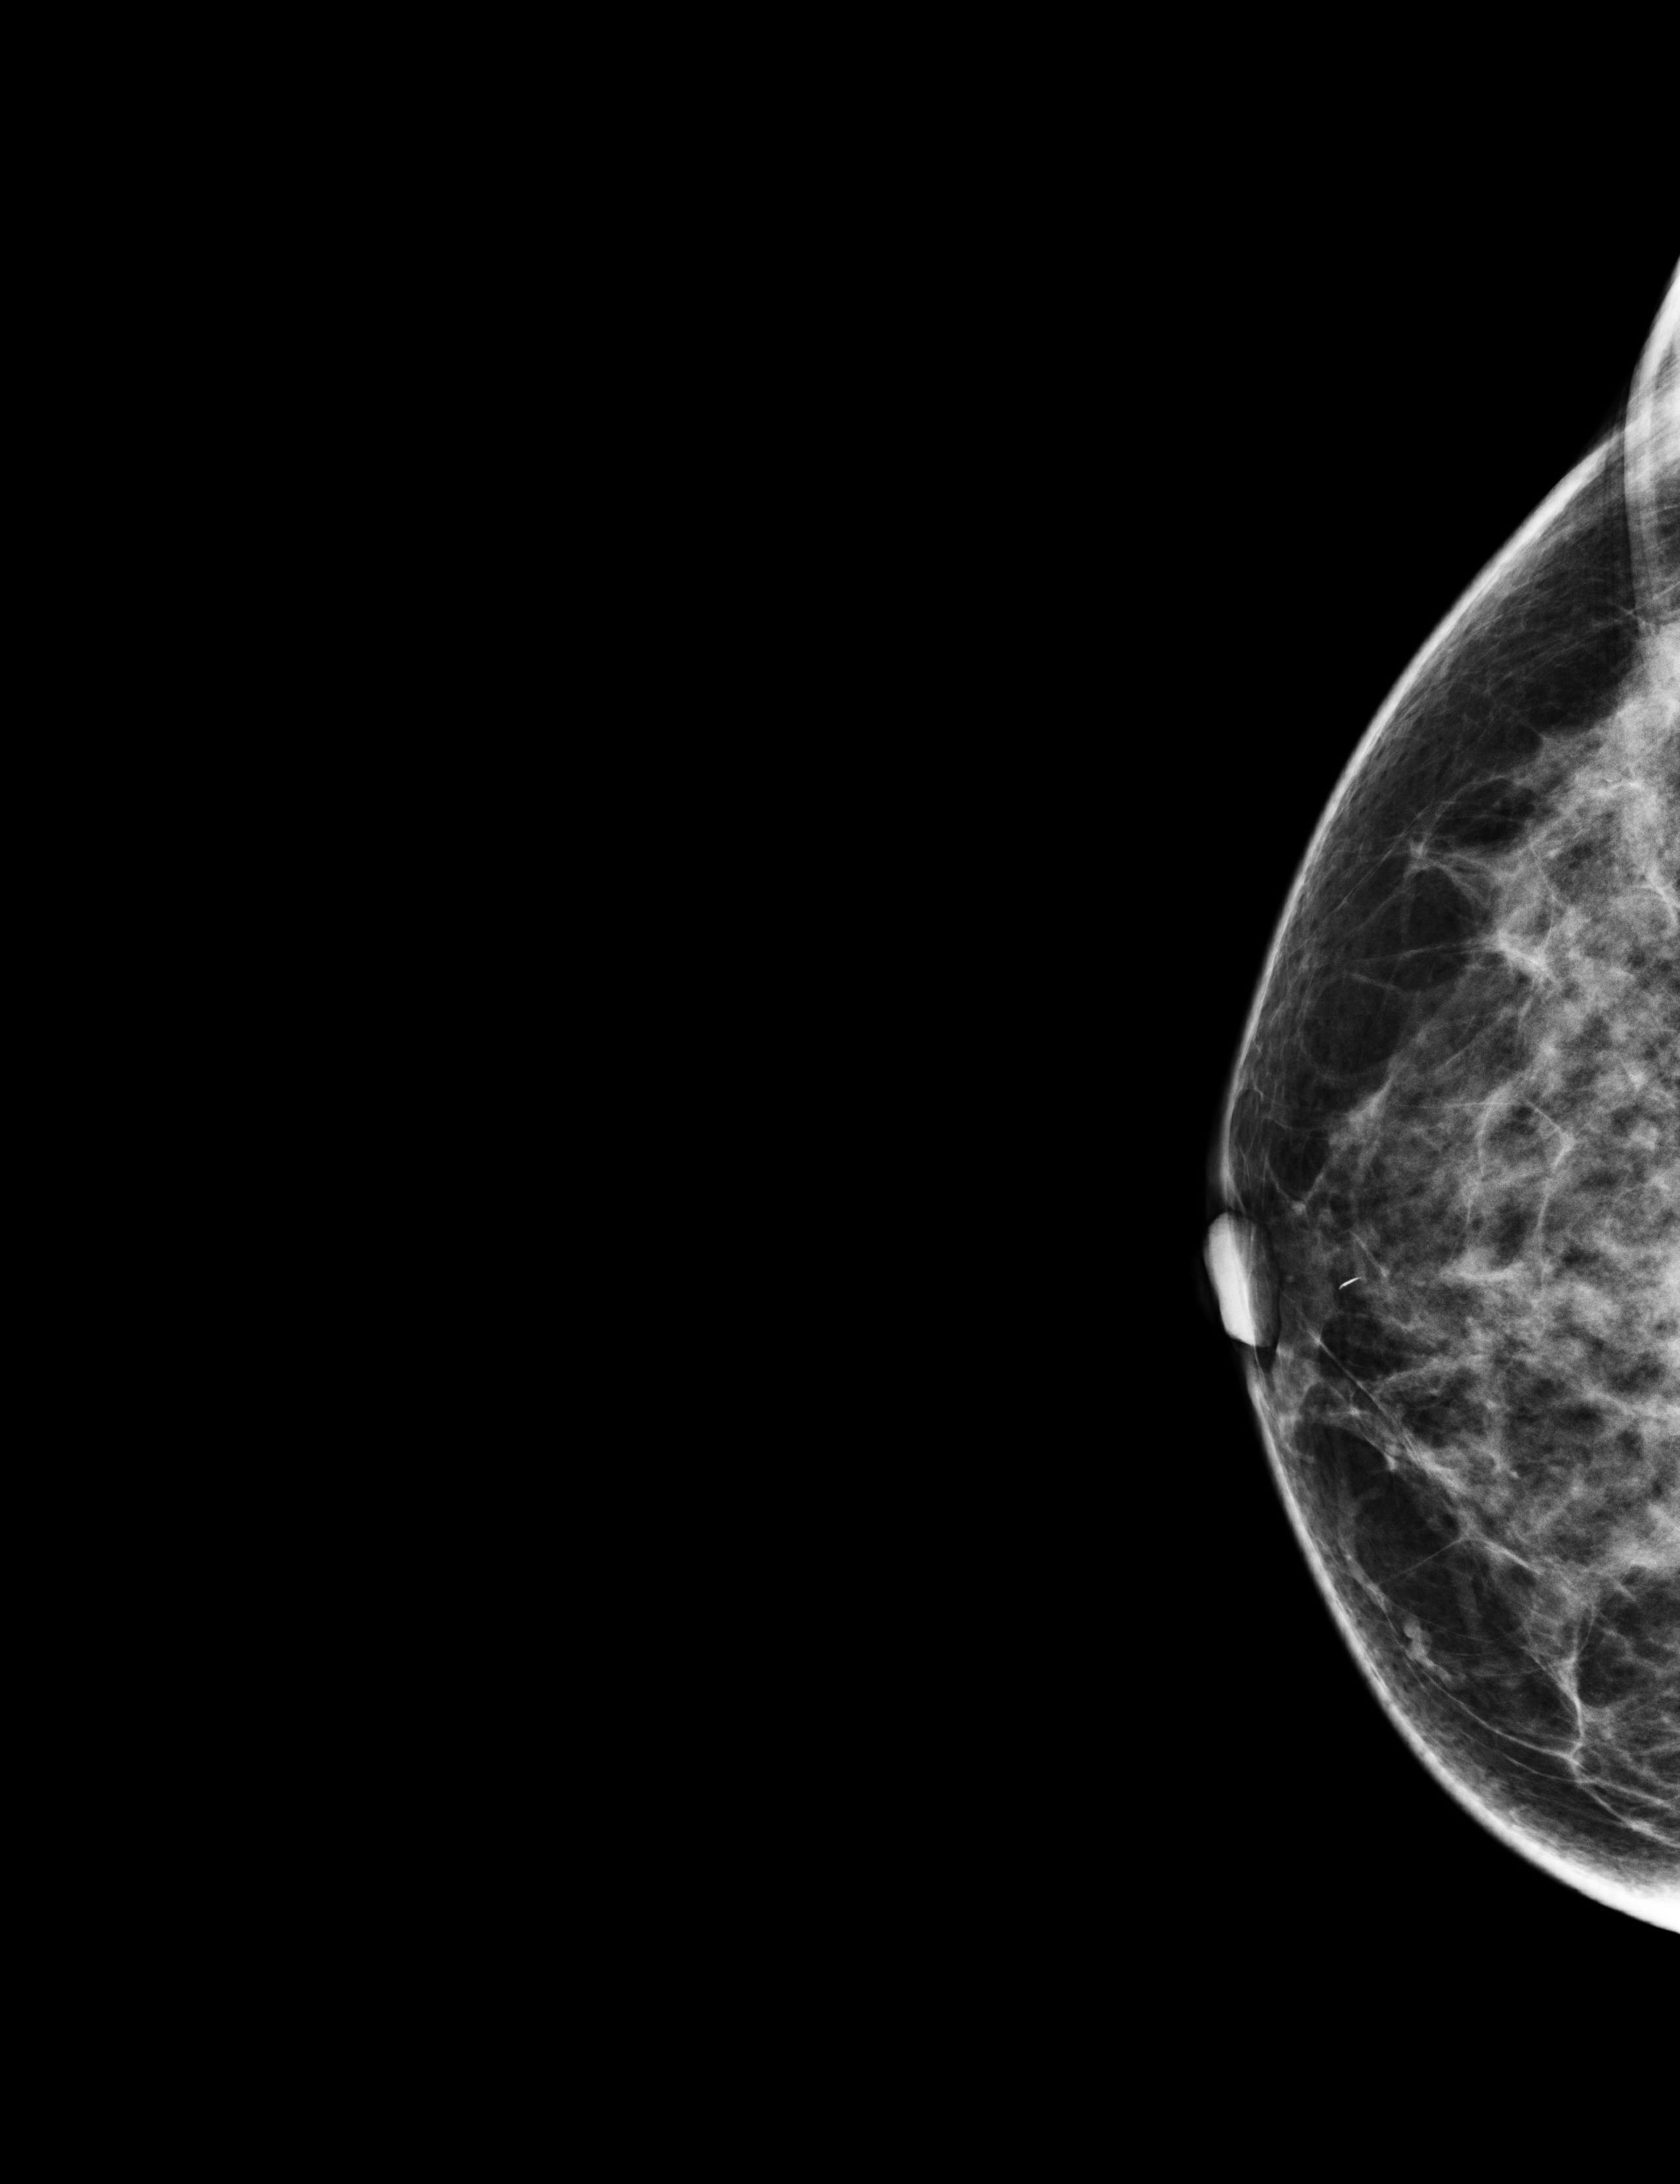
Digital mammogram (FFDM); right breast; cranio-caudal projection; annual screening mammography examination; compressed breast thickness 58 mm. Patient aged 54 years (female).
Final BI-RADS category for the screening round (tomosynthesis exam, both breasts): category 1.